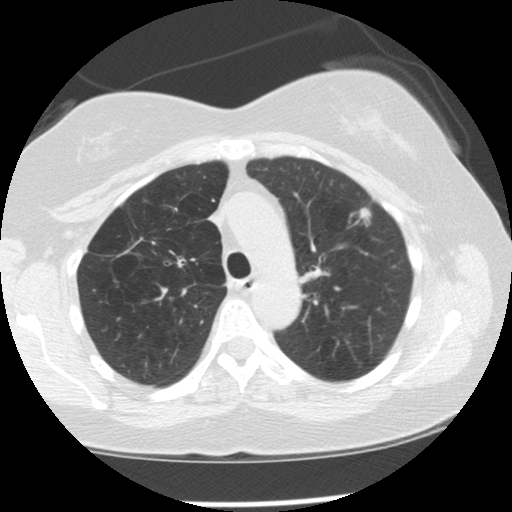
Axial slice from a low-dose chest CT screening exam; second screening round (one year after baseline); lung window (W 1500 / L -600 HU); 2.5 mm slice thickness; slice 38 of 128 in the series; 512 × 512 image matrix. Female, age 57 years at enrolment. Former smoker at enrolment.
Lesion marked by an expert reader, box from (x=342, y=201) to (x=381, y=235) px. The exam's reader record, not a measurement of the box and not confirmed to be the same lesion: non-calcified nodule or mass ≥4 mm, left upper lobe, 11 × 7 mm, spiculated (stellate) margins, soft tissue attenuation, pre-existing on the prior screen: yes; interval growth: yes. Official screen result: positive, change unspecified: nodule(s) >= 4 mm or enlarging nodule(s), mass(es), or other non-specific abnormalities suspicious for lung cancer.